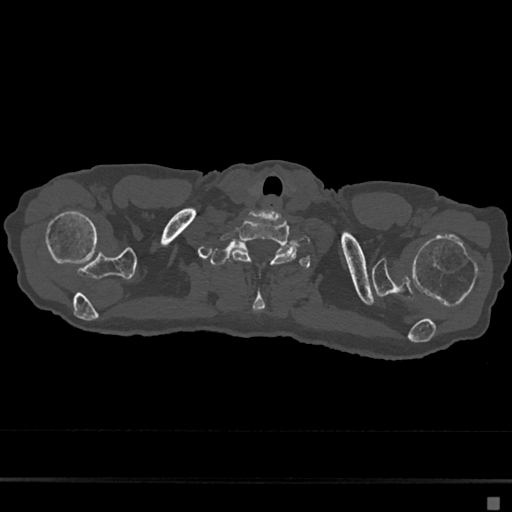
CT including the spine, one axial slice. Position 629 of 797 along the scan axis. Reconstruction kernel Br40s/3. 120 kVp. Bone window (W 1800 / L 400 HU). 0.5 mm slice thickness. 512 × 512 image matrix. Female patient, age 68 years. From the clinical record (not read from this slice): primary cancer: renal.
Annotated regions visible in this slice (semi-automatically segmented with operator editing):
- T1 vertebra: bounding box [x1, y1, x2, y2] px = [209, 241, 311, 312]